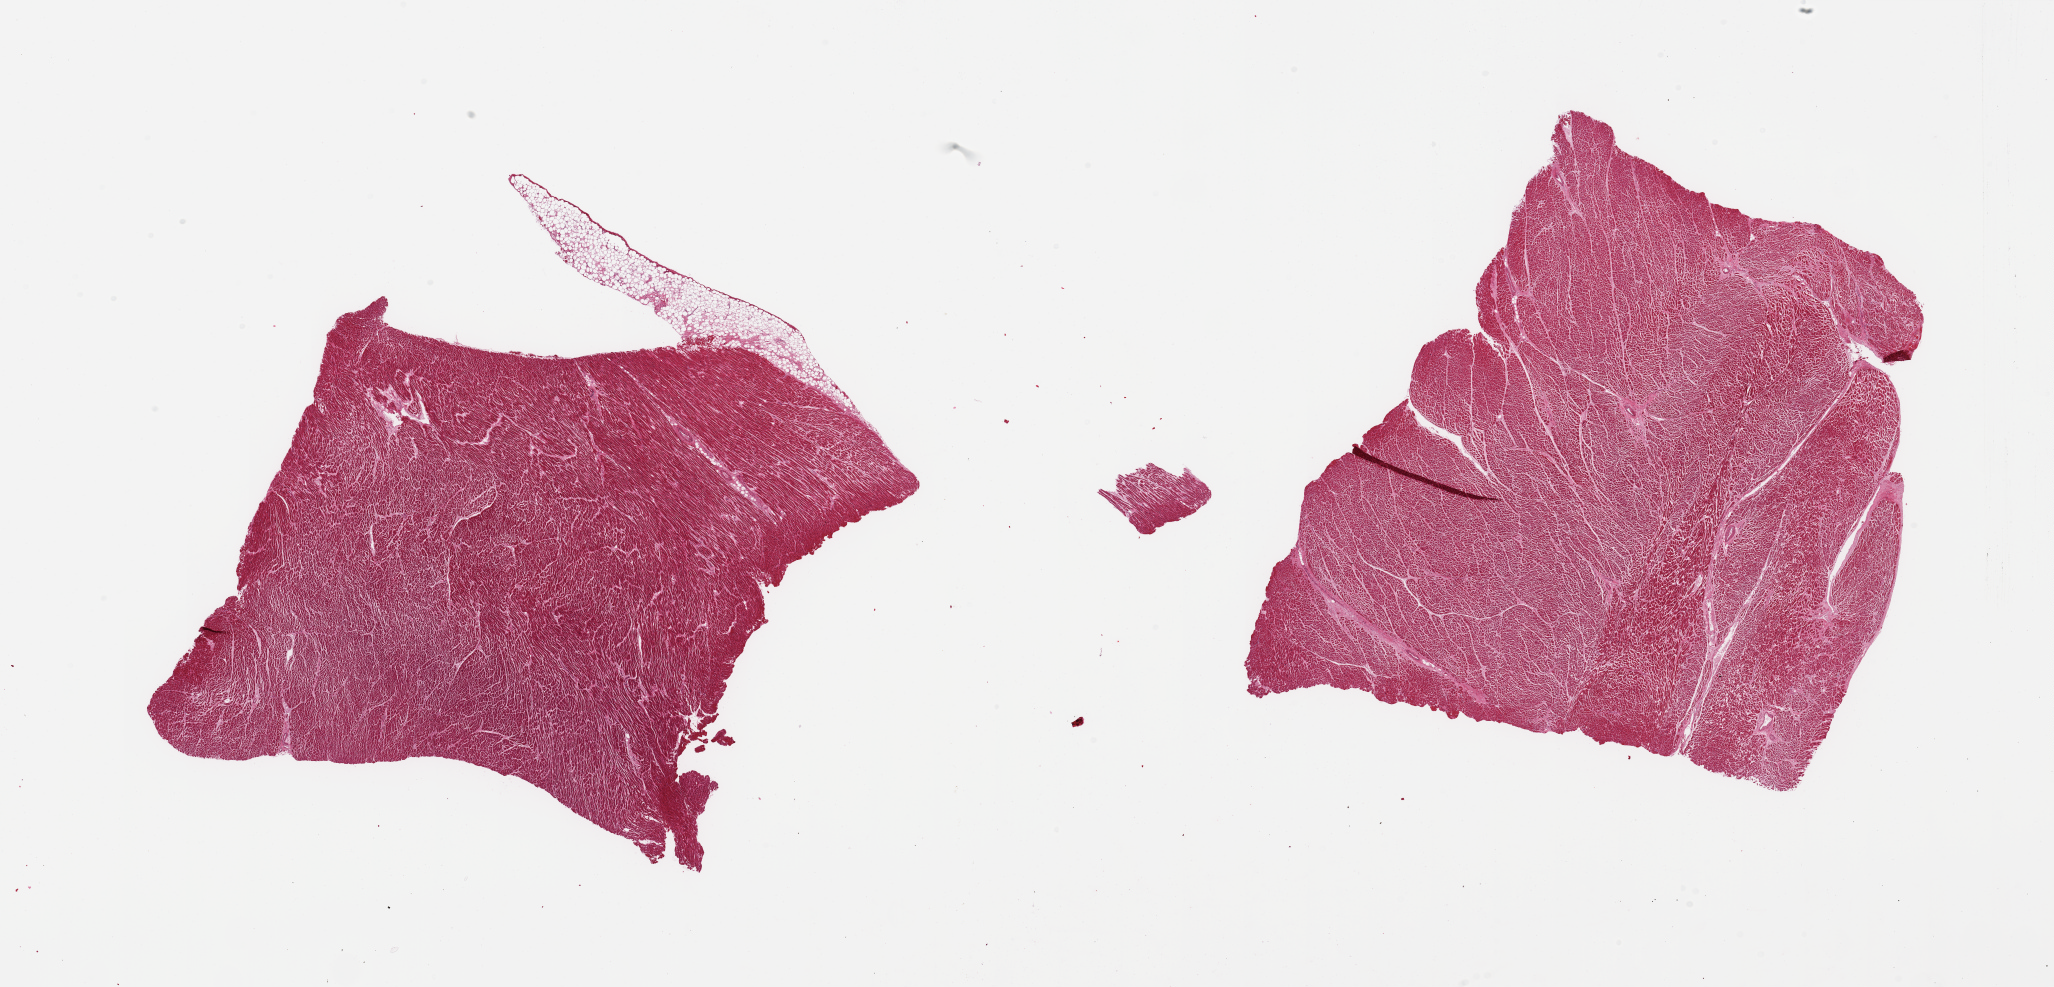
Digitized haematoxylin and eosin-stained section — whole scanned area (about 32.5 x 15.6 mm, acquisition: 20x scan) shown as a low-resolution overview, PAXgene-fixed, paraffin-embedded tissue, section of heart (target tissue), donor tissue sample. Male donor.
Reviewer comment on this tissue sample: 2 pieces; interstitial fibrosis.